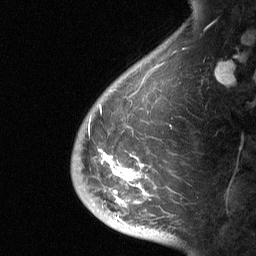
Breast MRI (dynamic contrast-enhanced), one sagittal slice; position 12 of 64 along the scan axis; dynamic contrast-enhanced study with each time point stored as its own series, time point 2 of 3 at this slice position (early post-contrast, ordered by acquisition time); 1.5 T; TE 4.8 ms, TR 27 ms; 2 mm slice thickness; 256 × 256 image matrix, field of view 180 × 180 mm. Patient: female, 56 years. Case-level facts recorded for this patient, not image findings: setting: breast cancer imaged before/during neoadjuvant chemotherapy; receptor status: HER2-positive.
Outlined on this slice (semi-automatic segmentation, software-assisted and operator-edited):
- analysis volume of interest (the breast-tissue region the enhancement analysis was run in; not a lesion): box from (x=71, y=142) to (x=182, y=229) px
- tumour enhancement mask (voxels above the 90 % enhancement threshold inside the analysis volume of interest): (x=99, y=148)–(x=145, y=219)